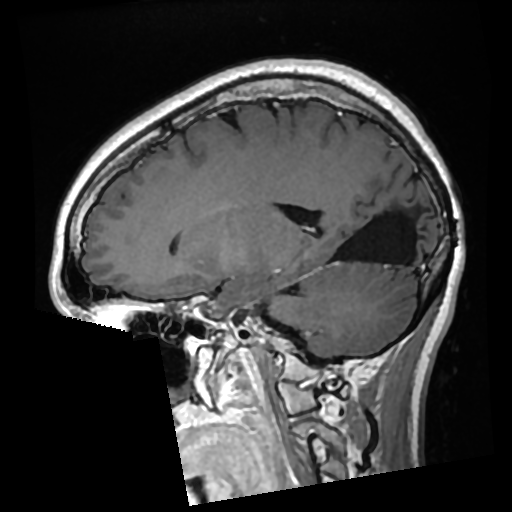
Brain MRI from a brain-tumour surgery series, one sagittal slice. T1-weighted post-contrast. 512 × 512 image matrix, field of view 250 × 250 mm. Case-level facts recorded for this patient, not image findings: histopathology: Glioma with ependymal features; WHO grade: 2; tumour location: Left Parietal.
Outlined on this slice (manually delineated by an expert):
- previous resection cavity: box from (x=336, y=194) to (x=422, y=264) px